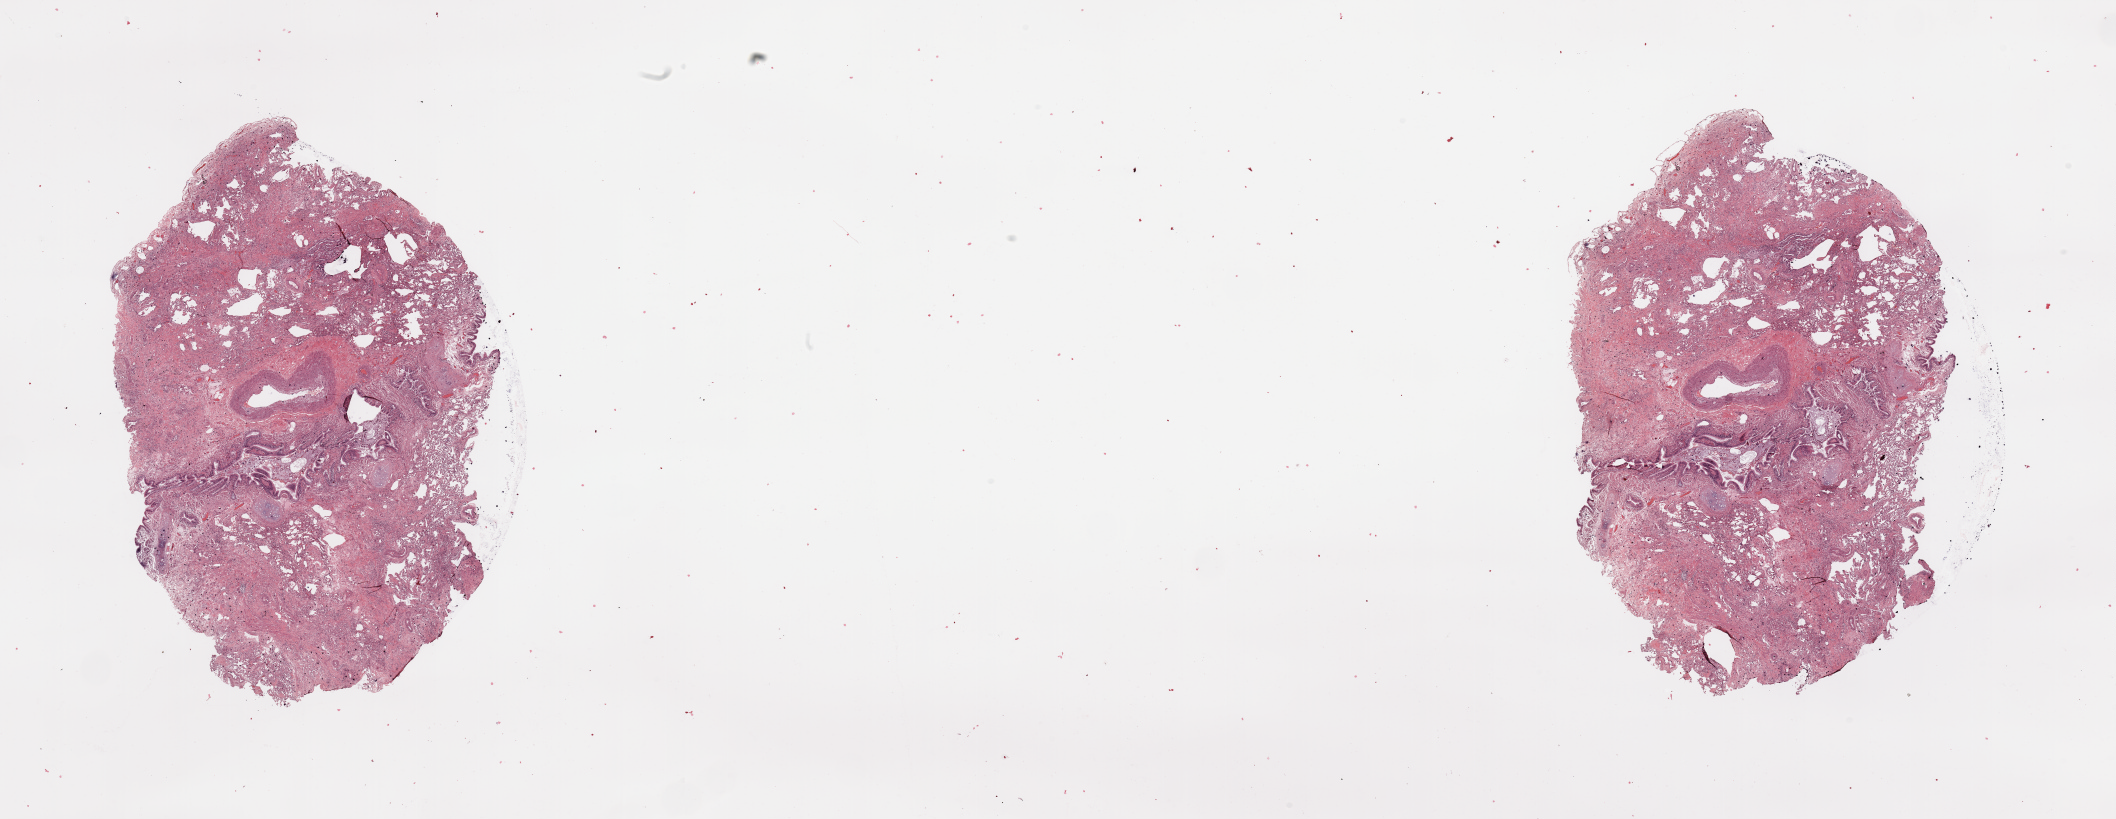
H&E-stained whole-slide image, shown as a low-resolution overview of the whole scanned area (about 33.5 x 13.0 mm); normal (non-tumour) tissue sample, lung. Male, 68 y/o.
- this section: normal (non-tumour) tissue from the same patient
- patient diagnosis (cohort enrolment): squamous cell carcinoma (lung)